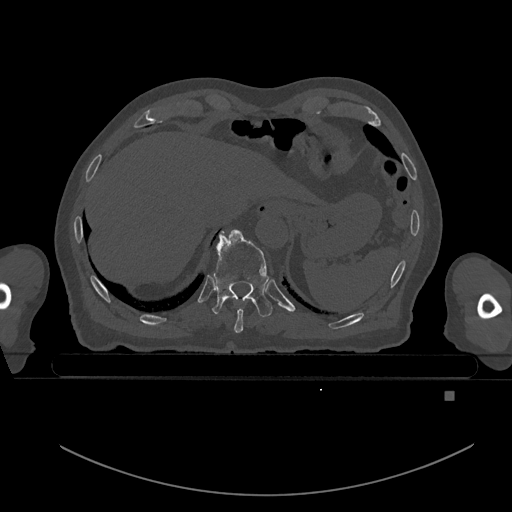
CT including the spine, one axial slice. Position 106 of 969 along the scan axis. Bone window (W 1800 / L 400 HU). 0.5 mm slice thickness. 512 × 512 image matrix, field of view 456 × 456 mm. Patient: male, 82 years. Case-level facts recorded for this patient, not image findings: primary cancer: prostate.
Structures marked on this image (semi-automatic segmentation, software-assisted and operator-edited):
- T10 vertebra: bounding box <213,229,273,317> (left, top, right, bottom; pixels)
- T9 vertebra: <234,304,244,333>